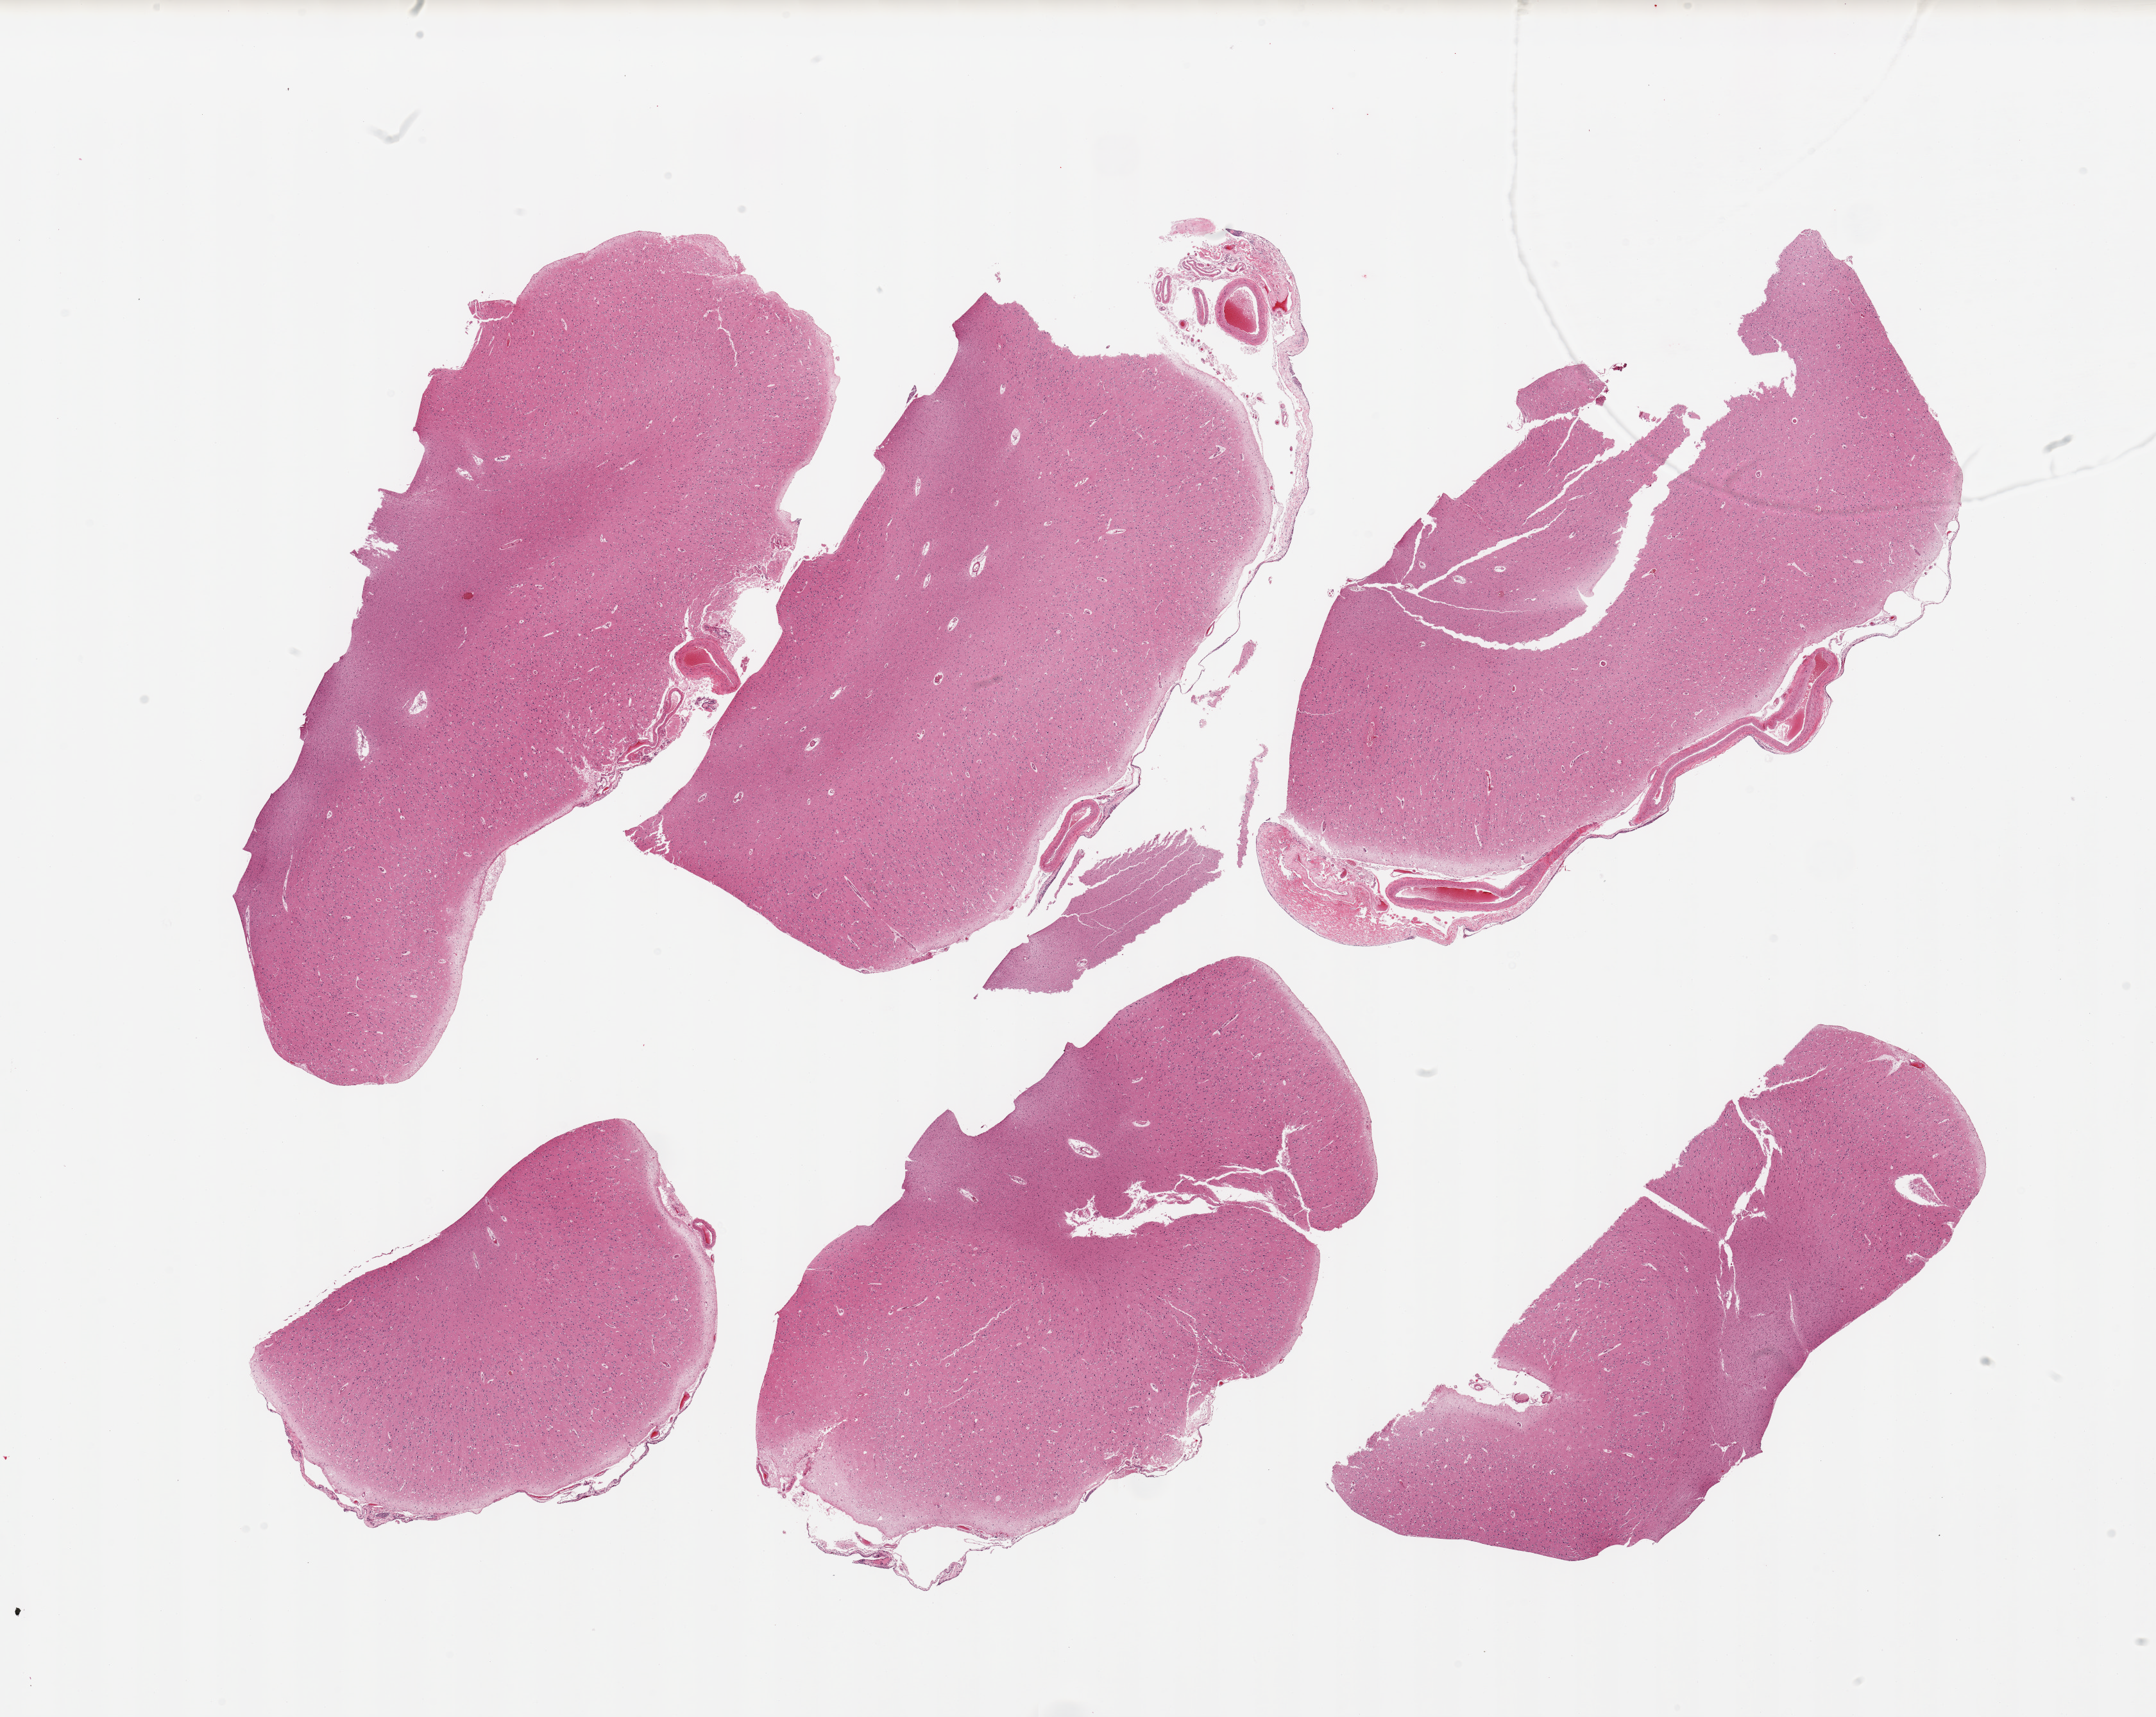
Whole-slide image, haematoxylin and eosin stain, brightfield — a low-resolution overview of the entire scanned area, about 26.6 x 21.2 mm (slide scanned at 20x); PAXgene-fixed paraffin-embedded (PFPE) section; sampled site (target tissue): cerebral cortex; tissue donor sample. Donor sex: male.
- reviewer comment on this tissue sample: 6 pieces, no abnormalities